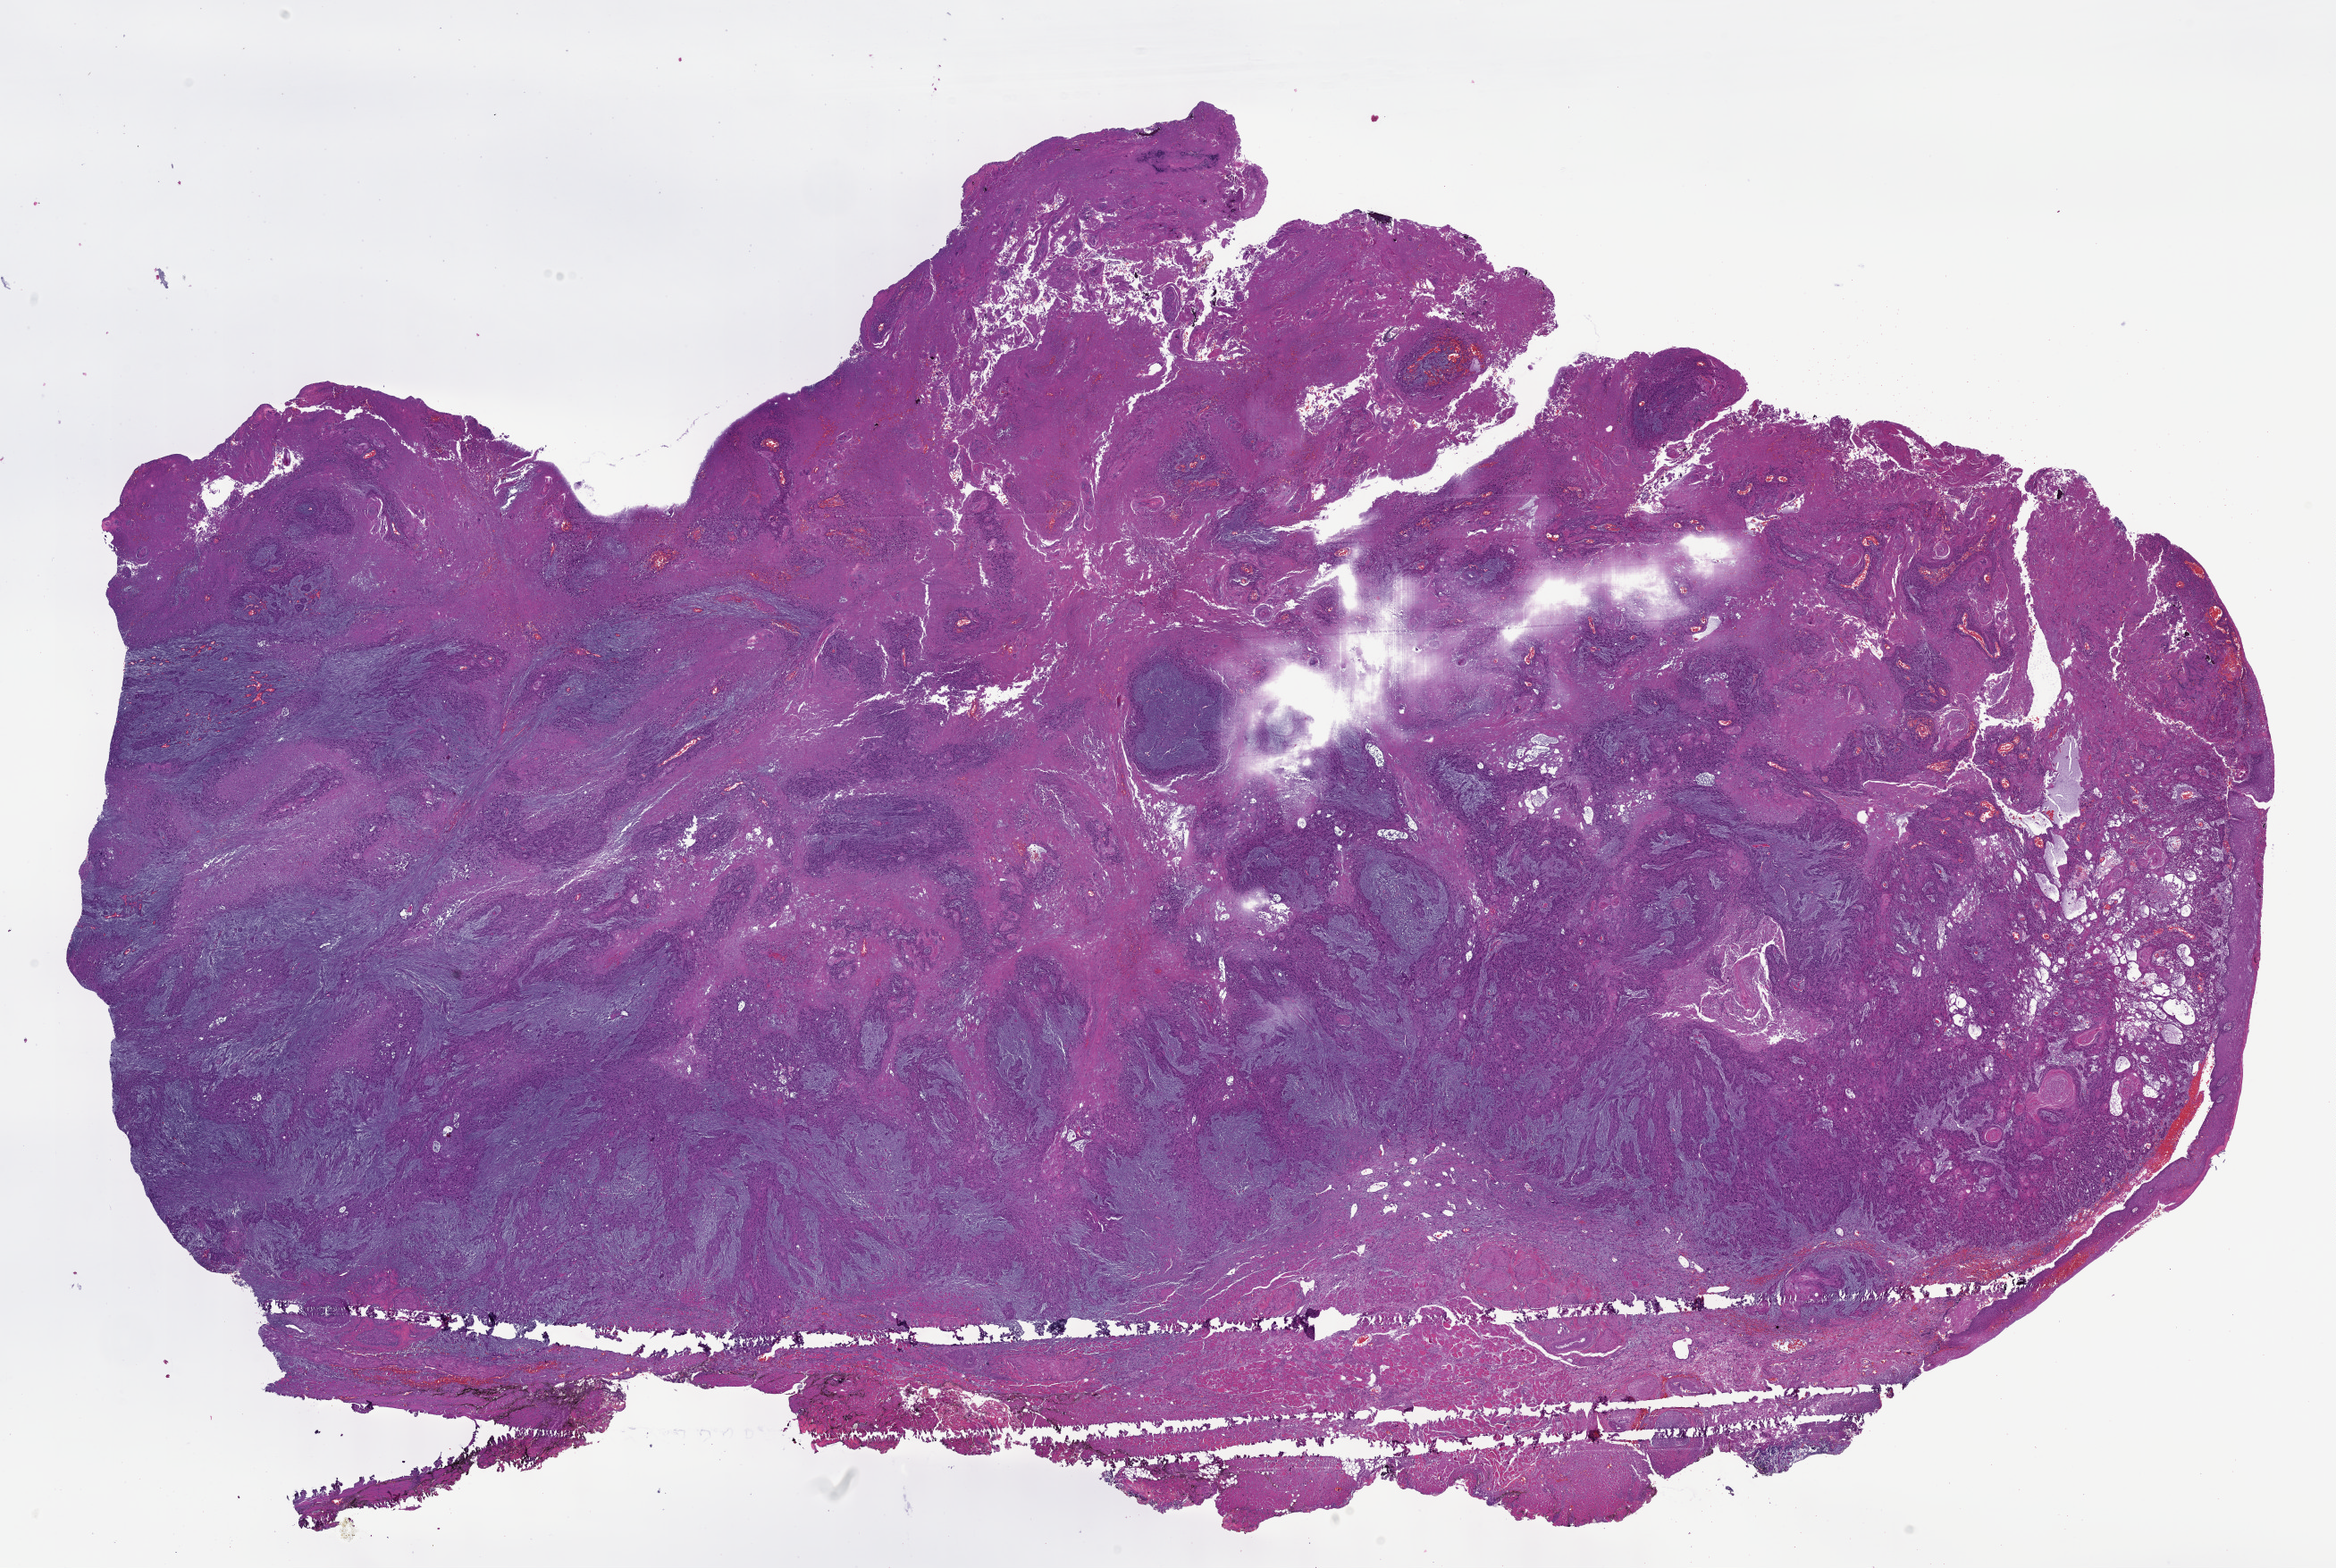
Whole-slide histology image, H&E-stained, whole scanned area (about 21.1 x 14.2 mm) shown as a low-resolution overview, formalin-fixed paraffin-embedded (FFPE) diagnostic section, primary tumour sample from the head and neck. Male, age 67 years at initial diagnosis. Histologic grade: G2 (moderately differentiated).
AJCC pathologic stage: III (7th edition). Diagnosis: Squamous cell carcinoma, NOS (tongue, NOS).